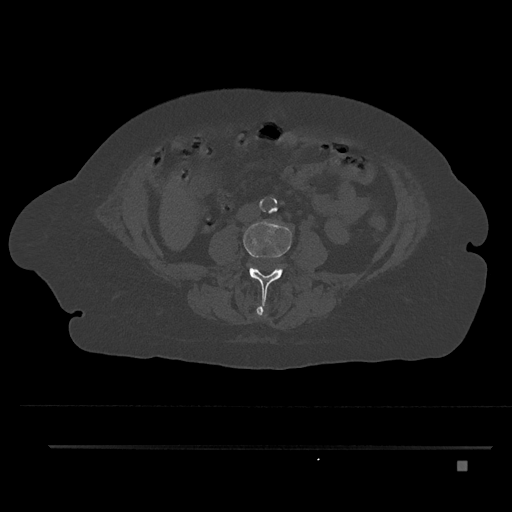
CT including the spine, one axial slice; slice 121 of 797 in the series (ordered by position); reconstruction kernel Br40s/3; 120 kVp; bone window (W 1800 / L 400 HU); 0.5 mm slice thickness; 512 × 512 image matrix. Patient: female, 76 years. From the clinical record (not read from this slice): primary cancer: lung; vertebrae with lytic lesions (as recorded): T11, L3.
Structures marked on this image (semi-automatic segmentation, software-assisted and operator-edited):
- L2 vertebra: bounding box <256,306,264,317> (left, top, right, bottom; pixels)
- L3 vertebra: <244,220,292,306>